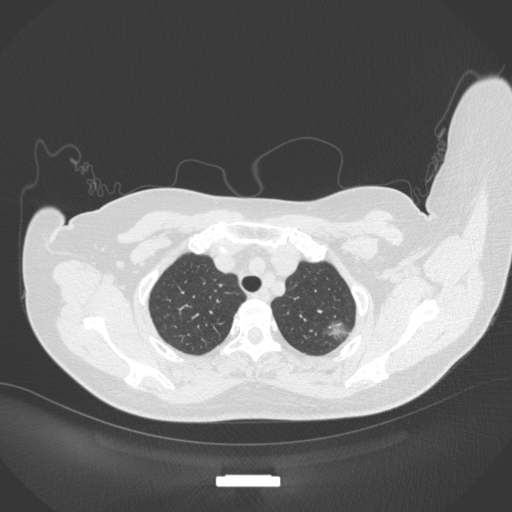
Chest CT, one axial slice. Slice 313 of 386 in the series (ordered by position). Lung window (W 1500 / L -600 HU). 512 × 512 image matrix, field of view 400 × 400 mm. Patient: female, 58 years. Case-level facts recorded for this patient, not image findings: clinical TNM (as recorded): T1c N0 M0.
Annotated regions visible in this slice (bounding box drawn by a radiologist):
- lung tumour (recorded histology: adenocarcinoma): bounding box <325,314,354,341> (left, top, right, bottom; pixels)